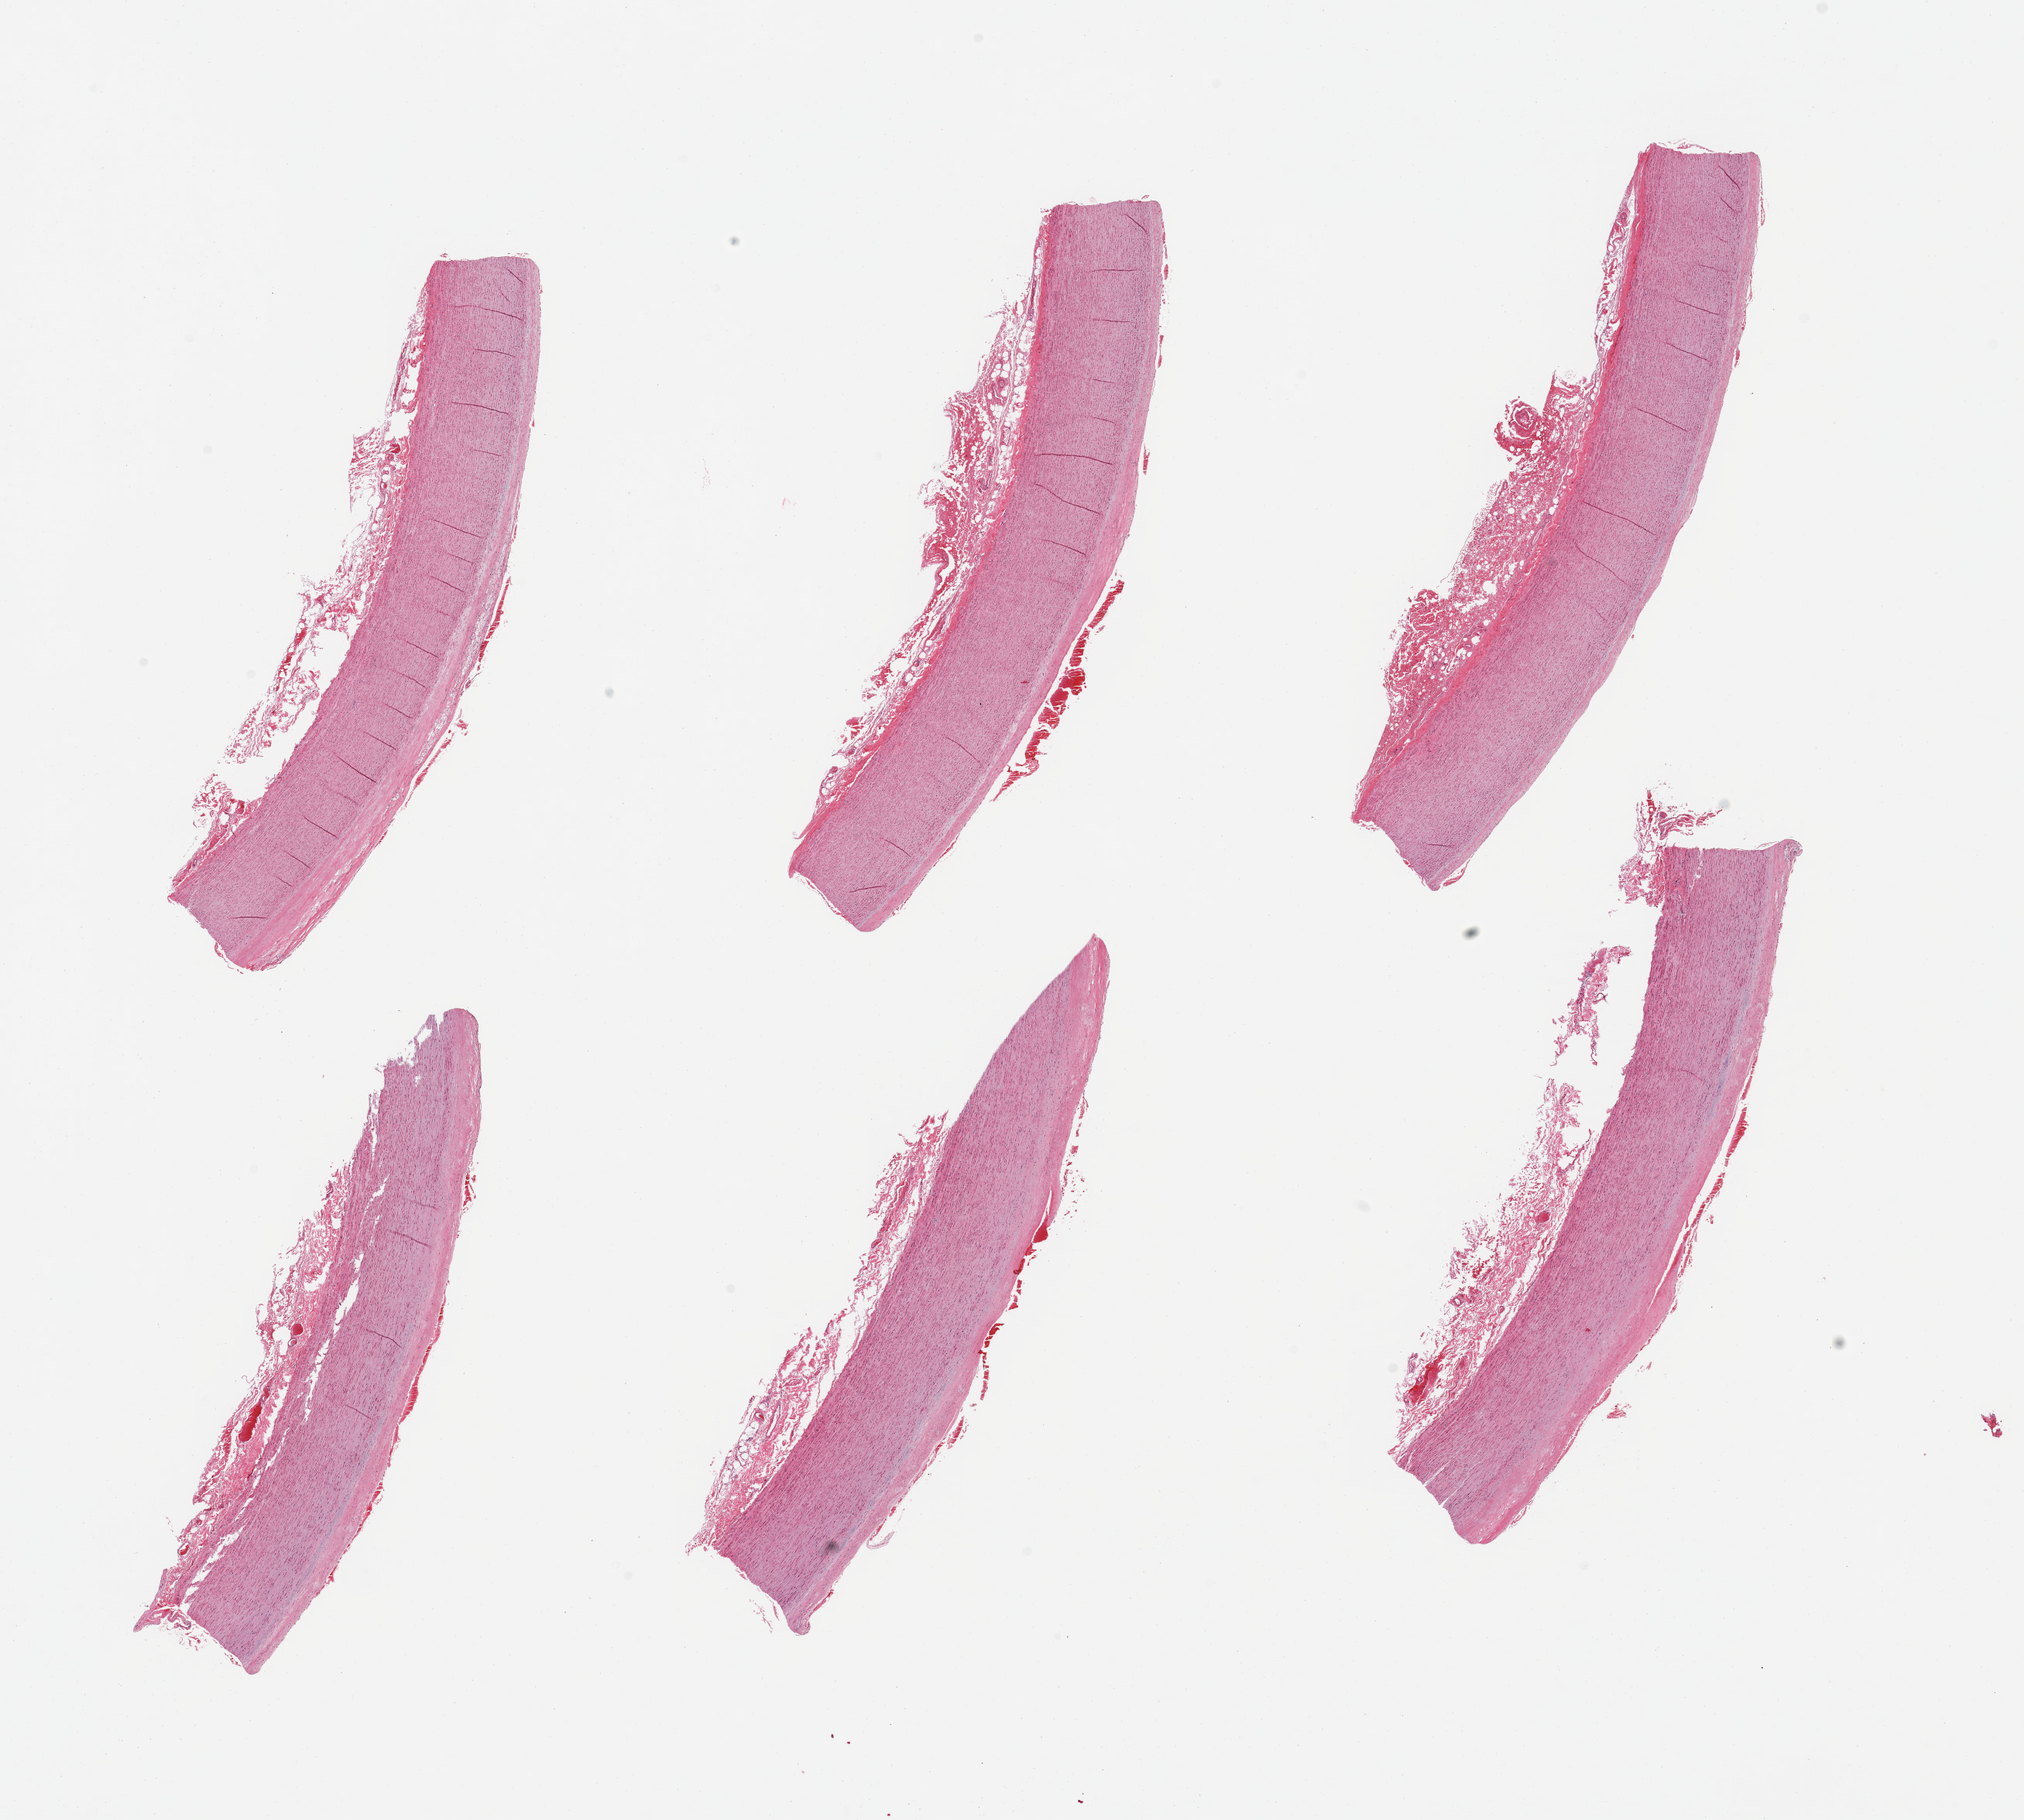
Digitized H&E-stained section, brightfield, whole scanned area (about 20.7 x 18.6 mm) shown as a low-resolution overview. PAXgene-fixed, paraffin-embedded tissue. Sampled site (target tissue): aorta. Donor tissue sample. Donor sex: female.
Pathologist's review note for this sample: 6 pieces; atherosclerotic plaque up to 0.4mm; attached adventitia up to ~0.85mm.